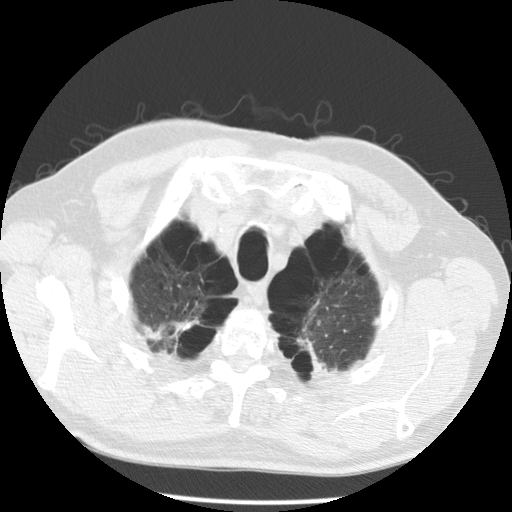
Axial slice from a low-dose chest CT screening exam, second screening round (one year after baseline), lung window (W 1500 / L -600 HU), 2.5 mm slice thickness, standard (soft-tissue) reconstruction kernel (STANDARD), 120 kVp. Male participant, aged 68 years at enrolment.
Expert reader's lesion annotation, bounding box [x1, y1, x2, y2] px = [129, 294, 203, 366]. The screening reader recorded 2 non-calcified nodules or masses ≥4 mm on this exam; which of them this box marks is not recorded. Official screen result: positive, no significant change: stable abnormalities potentially related to lung cancer, unchanged since the prior screening exam. Lung cancer was diagnosed 617 days after this screen: large cell carcinoma, NOS, right upper lobe, poorly differentiated (G3), stage IV (AJCC 6th edition).